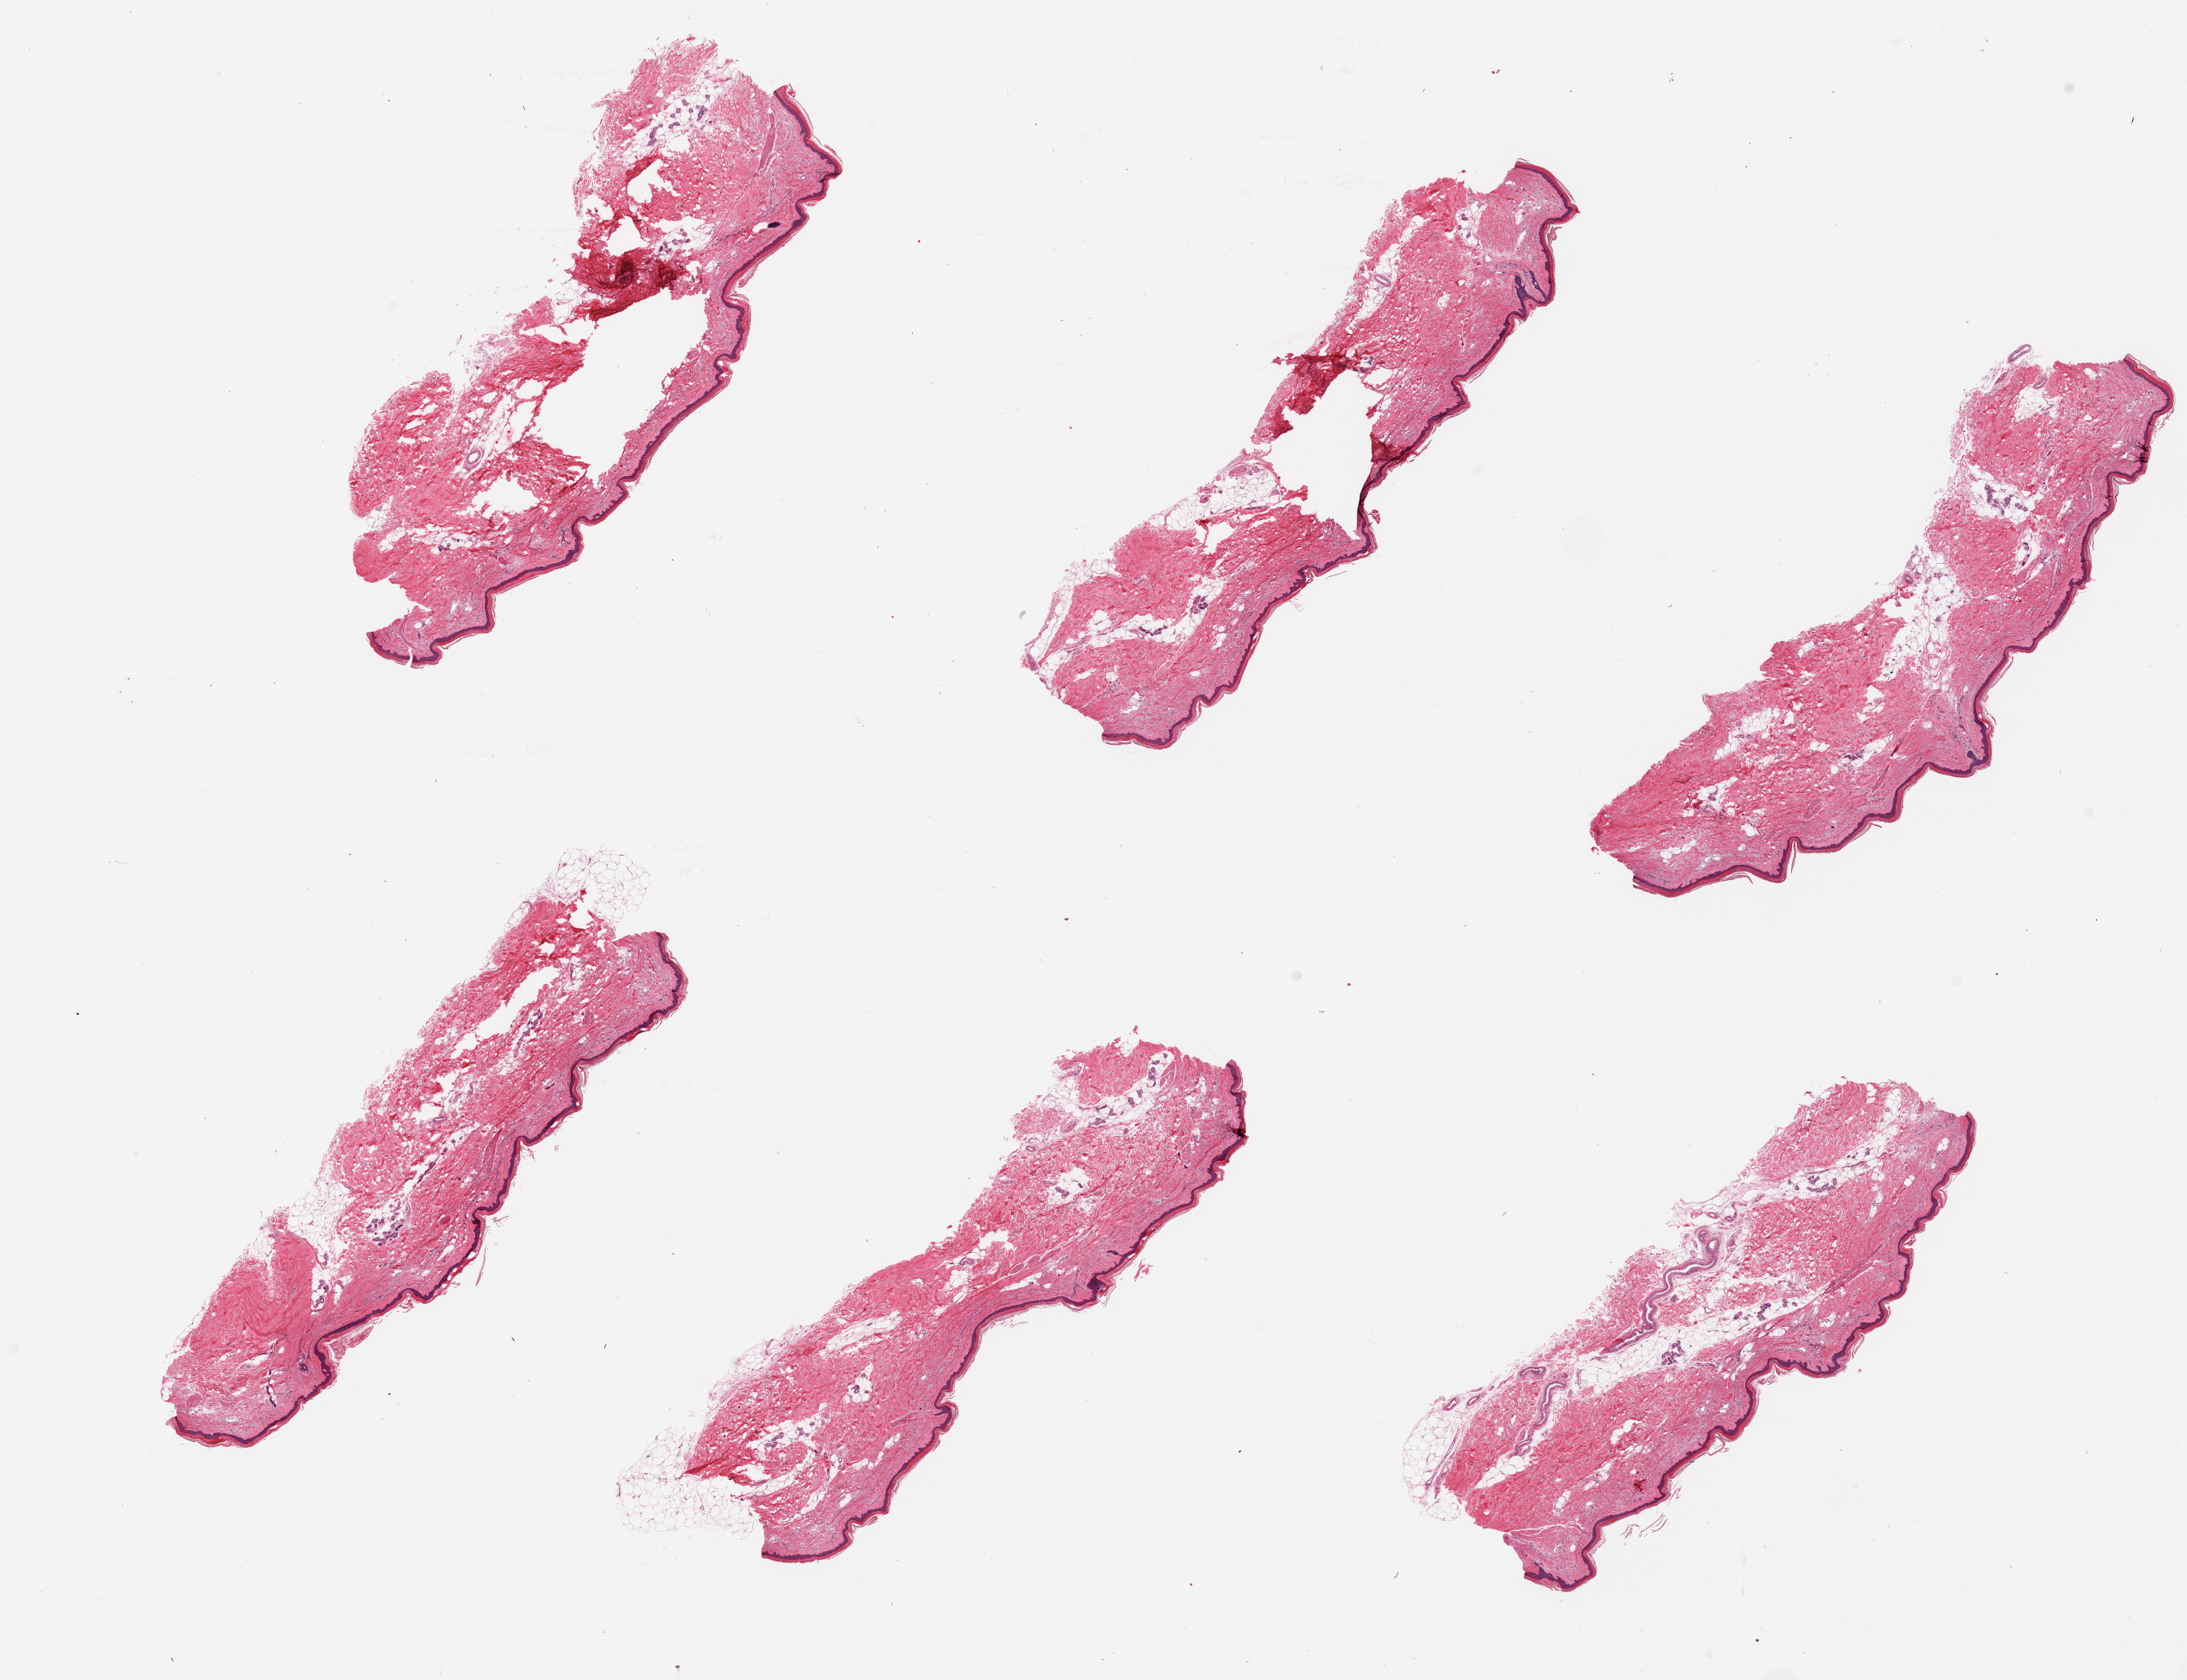
Whole-slide image, H&E stain — a low-resolution overview of the entire scanned area, about 22.6 x 17.4 mm (slide scanned at 20x); PAXgene-fixed paraffin-embedded (PFPE) section; section of skin of lower leg (target tissue); donor tissue sample. Donor: female.
Pathologist's review note for this sample: 6 pieces, up to 8x2mm; well trimmed but with central holes (artifacts).